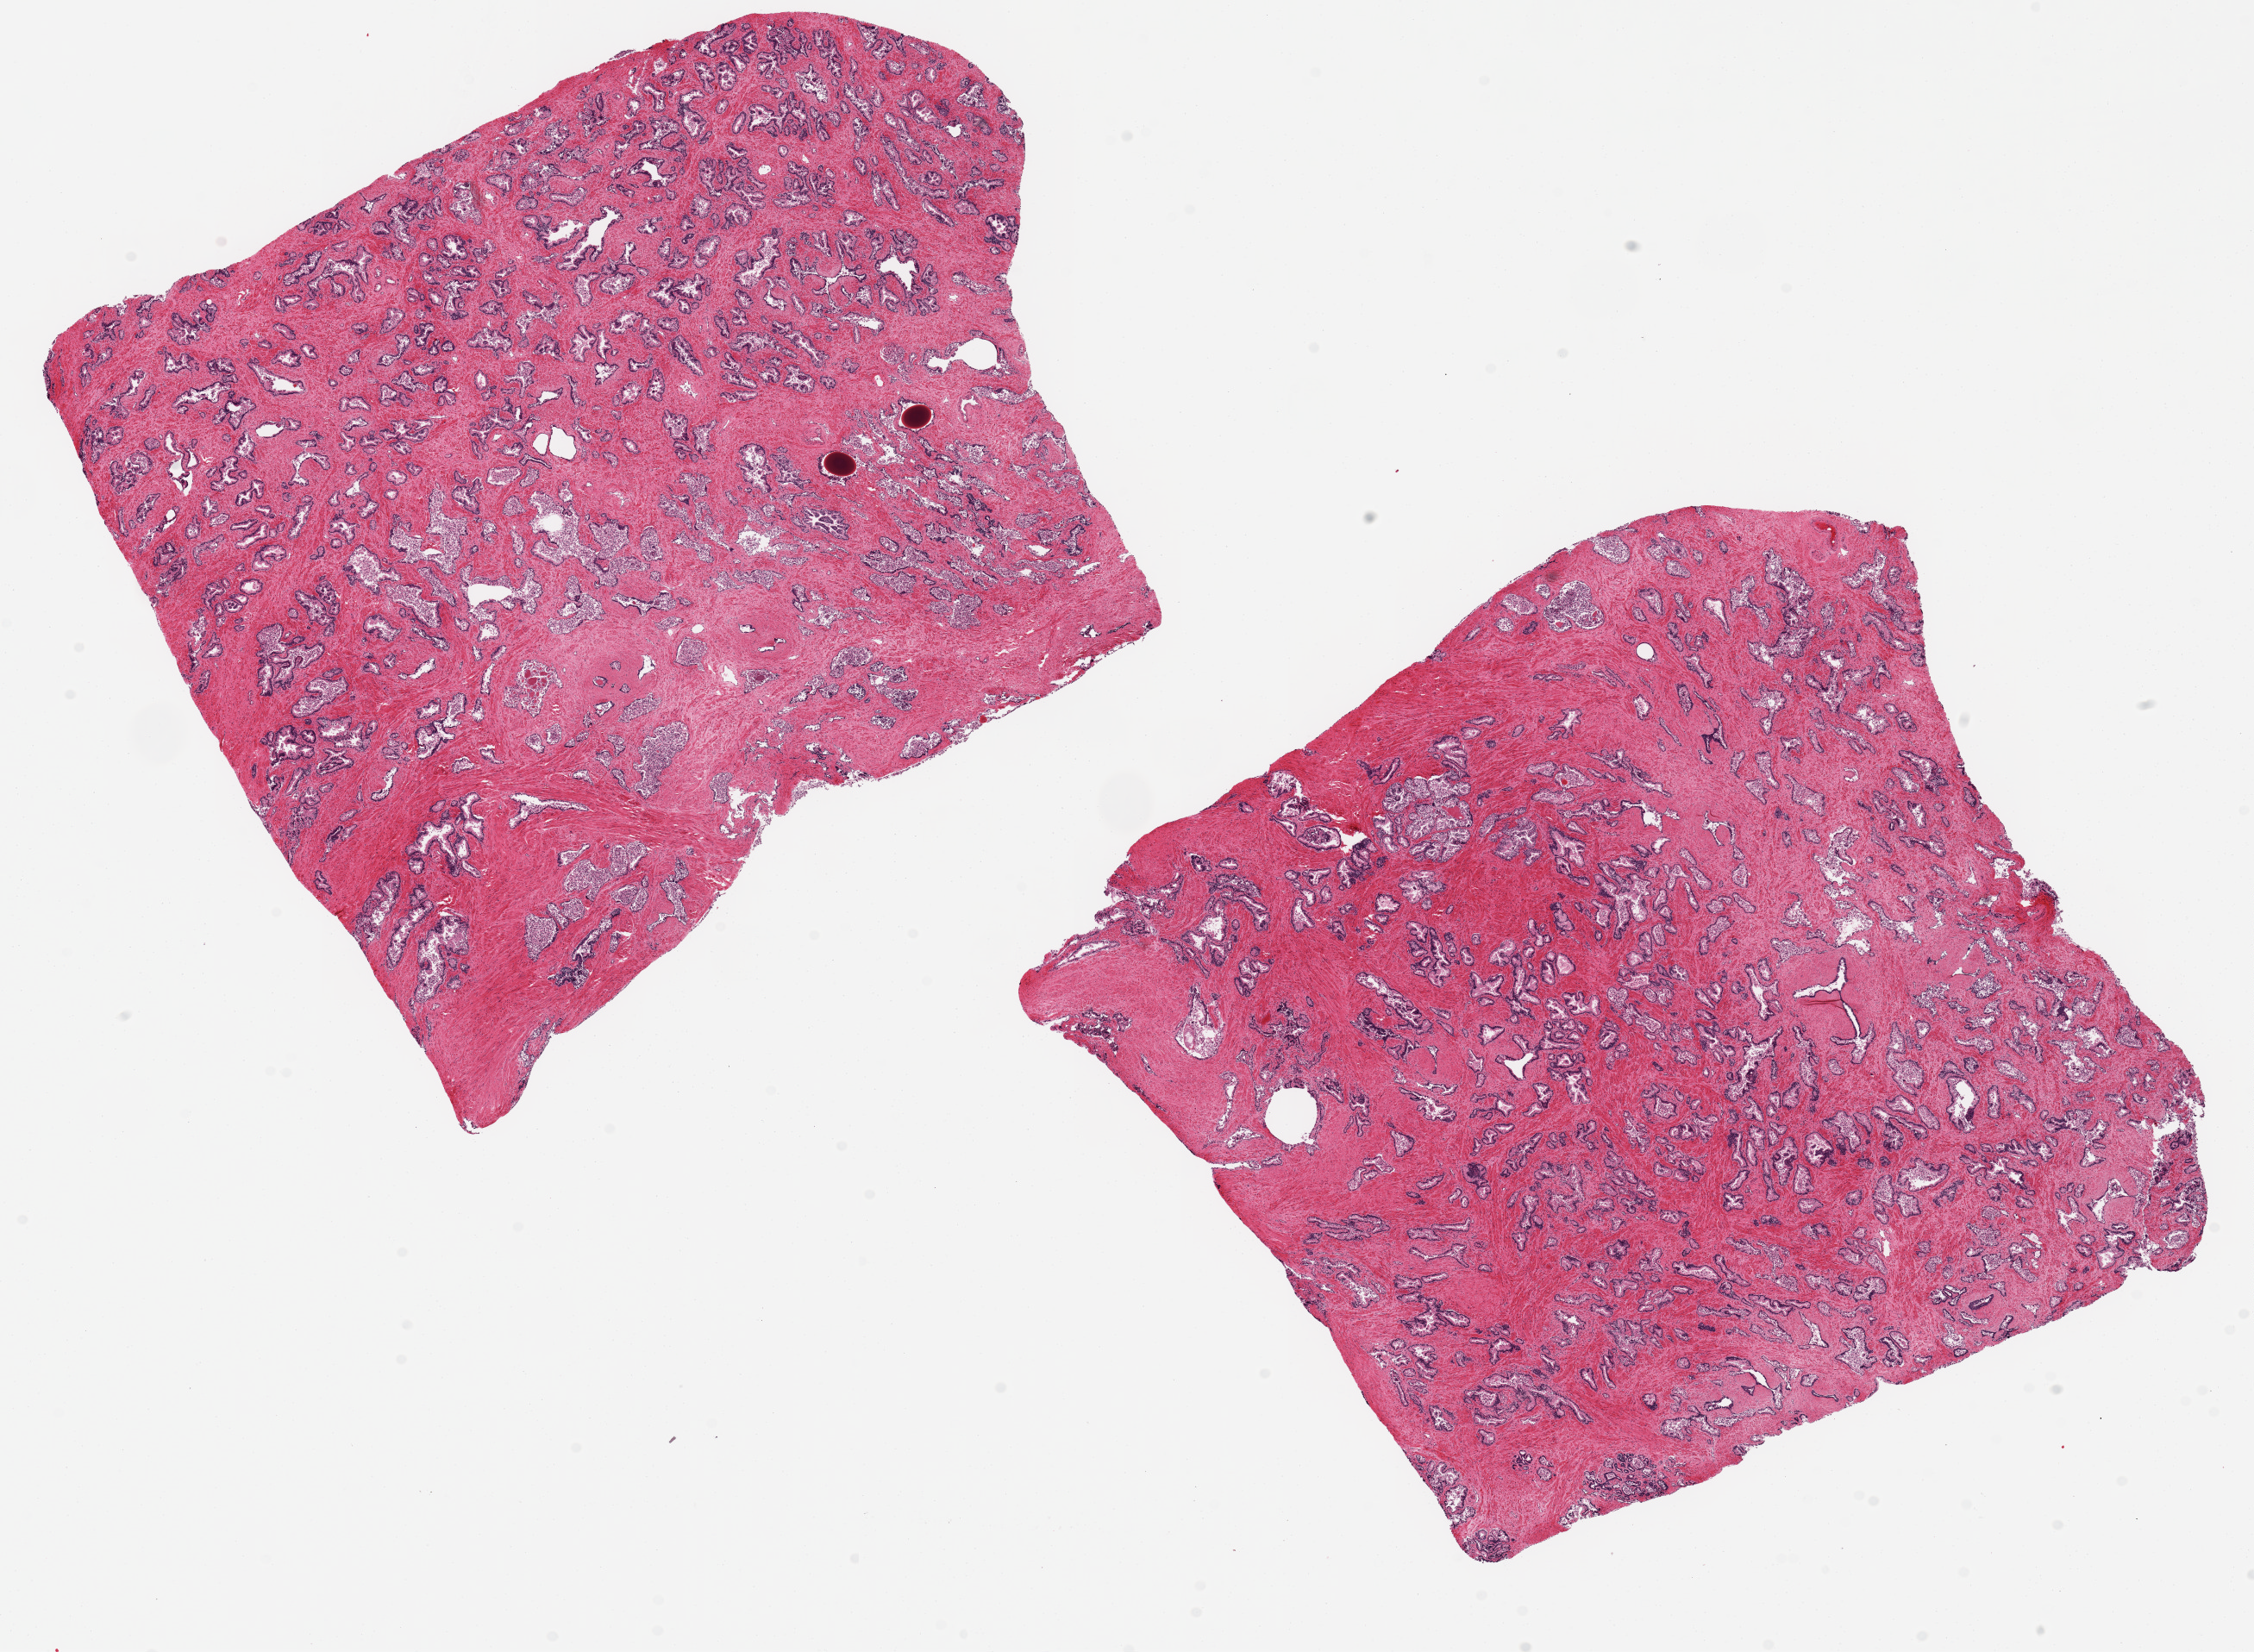
Digitized hematoxylin and eosin (H&E)-stained section, brightfield, a low-resolution overview of the entire scanned area, about 20.7 x 15.2 mm. PAXgene-fixed, paraffin-embedded tissue. Sampled site (target tissue): prostate. Donor tissue sample.
* review note (as recorded): 2 ~9x7.5mm aliquots; glandular mucosa badly autolyzed